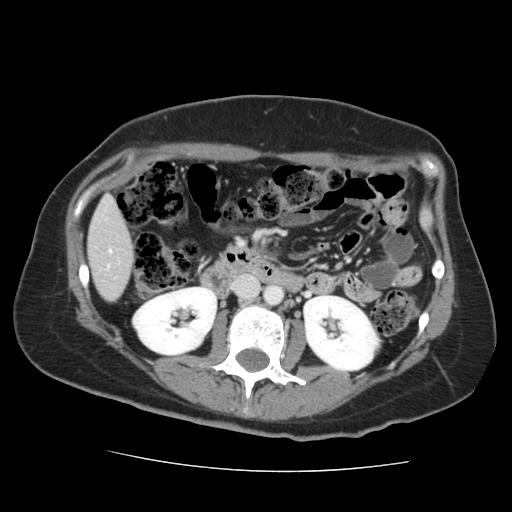
Contrast-enhanced abdominal CT, one axial slice; position 52 of 144 along the scan axis; 120 kVp; soft-tissue window (W 400 / L 40 HU); 2.5 mm slice thickness; 512 × 512 image matrix, field of view 333 × 333 mm. Female patient, age 46 years. Case-level facts recorded for this patient, not image findings: diagnosis: colorectal cancer liver metastases, imaged before liver resection; multiple liver metastases: no; largest metastasis: 2.8 cm.
Structures marked on this image (outlined manually by an expert reader):
- liver: box from (x=90, y=200) to (x=132, y=300) px
- planned liver remnant (the part of the liver to remain after resection): (x=90, y=200)–(x=132, y=294)
- portal vein (with intrahepatic branches): (x=109, y=250)–(x=111, y=253)